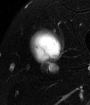
MRI of an extremity soft-tissue mass, one axial slice. Position 46 of 65 along the scan axis. T2-weighted fat-saturated. MR volume resampled by the dataset authors to the PET/CT grid (not the native acquisition matrix). 90 × 105 image matrix. Male patient. Case-level facts recorded for this patient, not image findings: histological type: mixoid liposarcoma; grade: low; site of the primary tumour: left thigh.
Structures marked on this image (expert contour drawn on MRI and transferred to this co-registered scan by the dataset authors):
- gross tumour volume (mass): bounding box <32,36,60,63> (left, top, right, bottom; pixels)